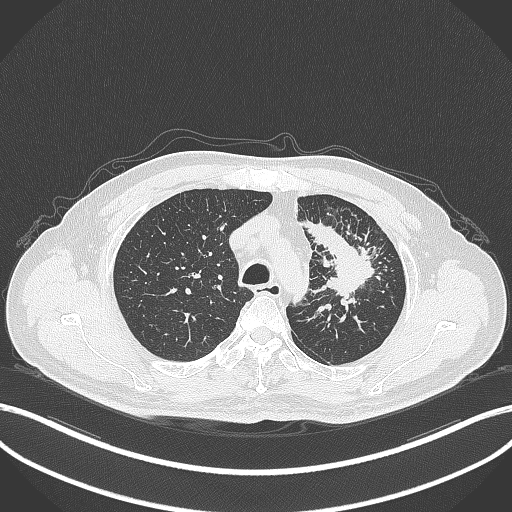
Chest CT, one axial slice; reconstruction kernel B70f; 120 kVp; lung window (W 1500 / L -600 HU); 1 mm slice thickness; 512 × 512 image matrix, field of view 400 × 400 mm. Patient: male, 69 years. Case-level facts recorded for this patient, not image findings: clinical TNM (as recorded): T2a N2 M0; histopathological grade: G2-3.
Outlined on this slice (bounding box drawn by a radiologist):
- lung tumour (recorded histology: adenocarcinoma): bounding box <302,217,382,311> (left, top, right, bottom; pixels)